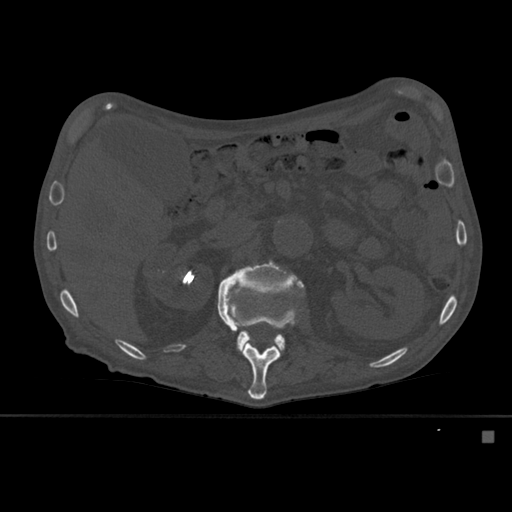
CT including the spine, one axial slice. Position 248 of 527 along the scan axis. Bone window (W 1800 / L 400 HU). 1.5 mm slice thickness. 512 × 512 image matrix. Male patient, age 78 years. From the clinical record (not read from this slice): primary cancer: prostate.
Structures marked on this image (semi-automatically segmented with operator editing):
- L1 vertebra: bounding box <217,281,298,400> (left, top, right, bottom; pixels)
- L2 vertebra: <219,259,304,352>